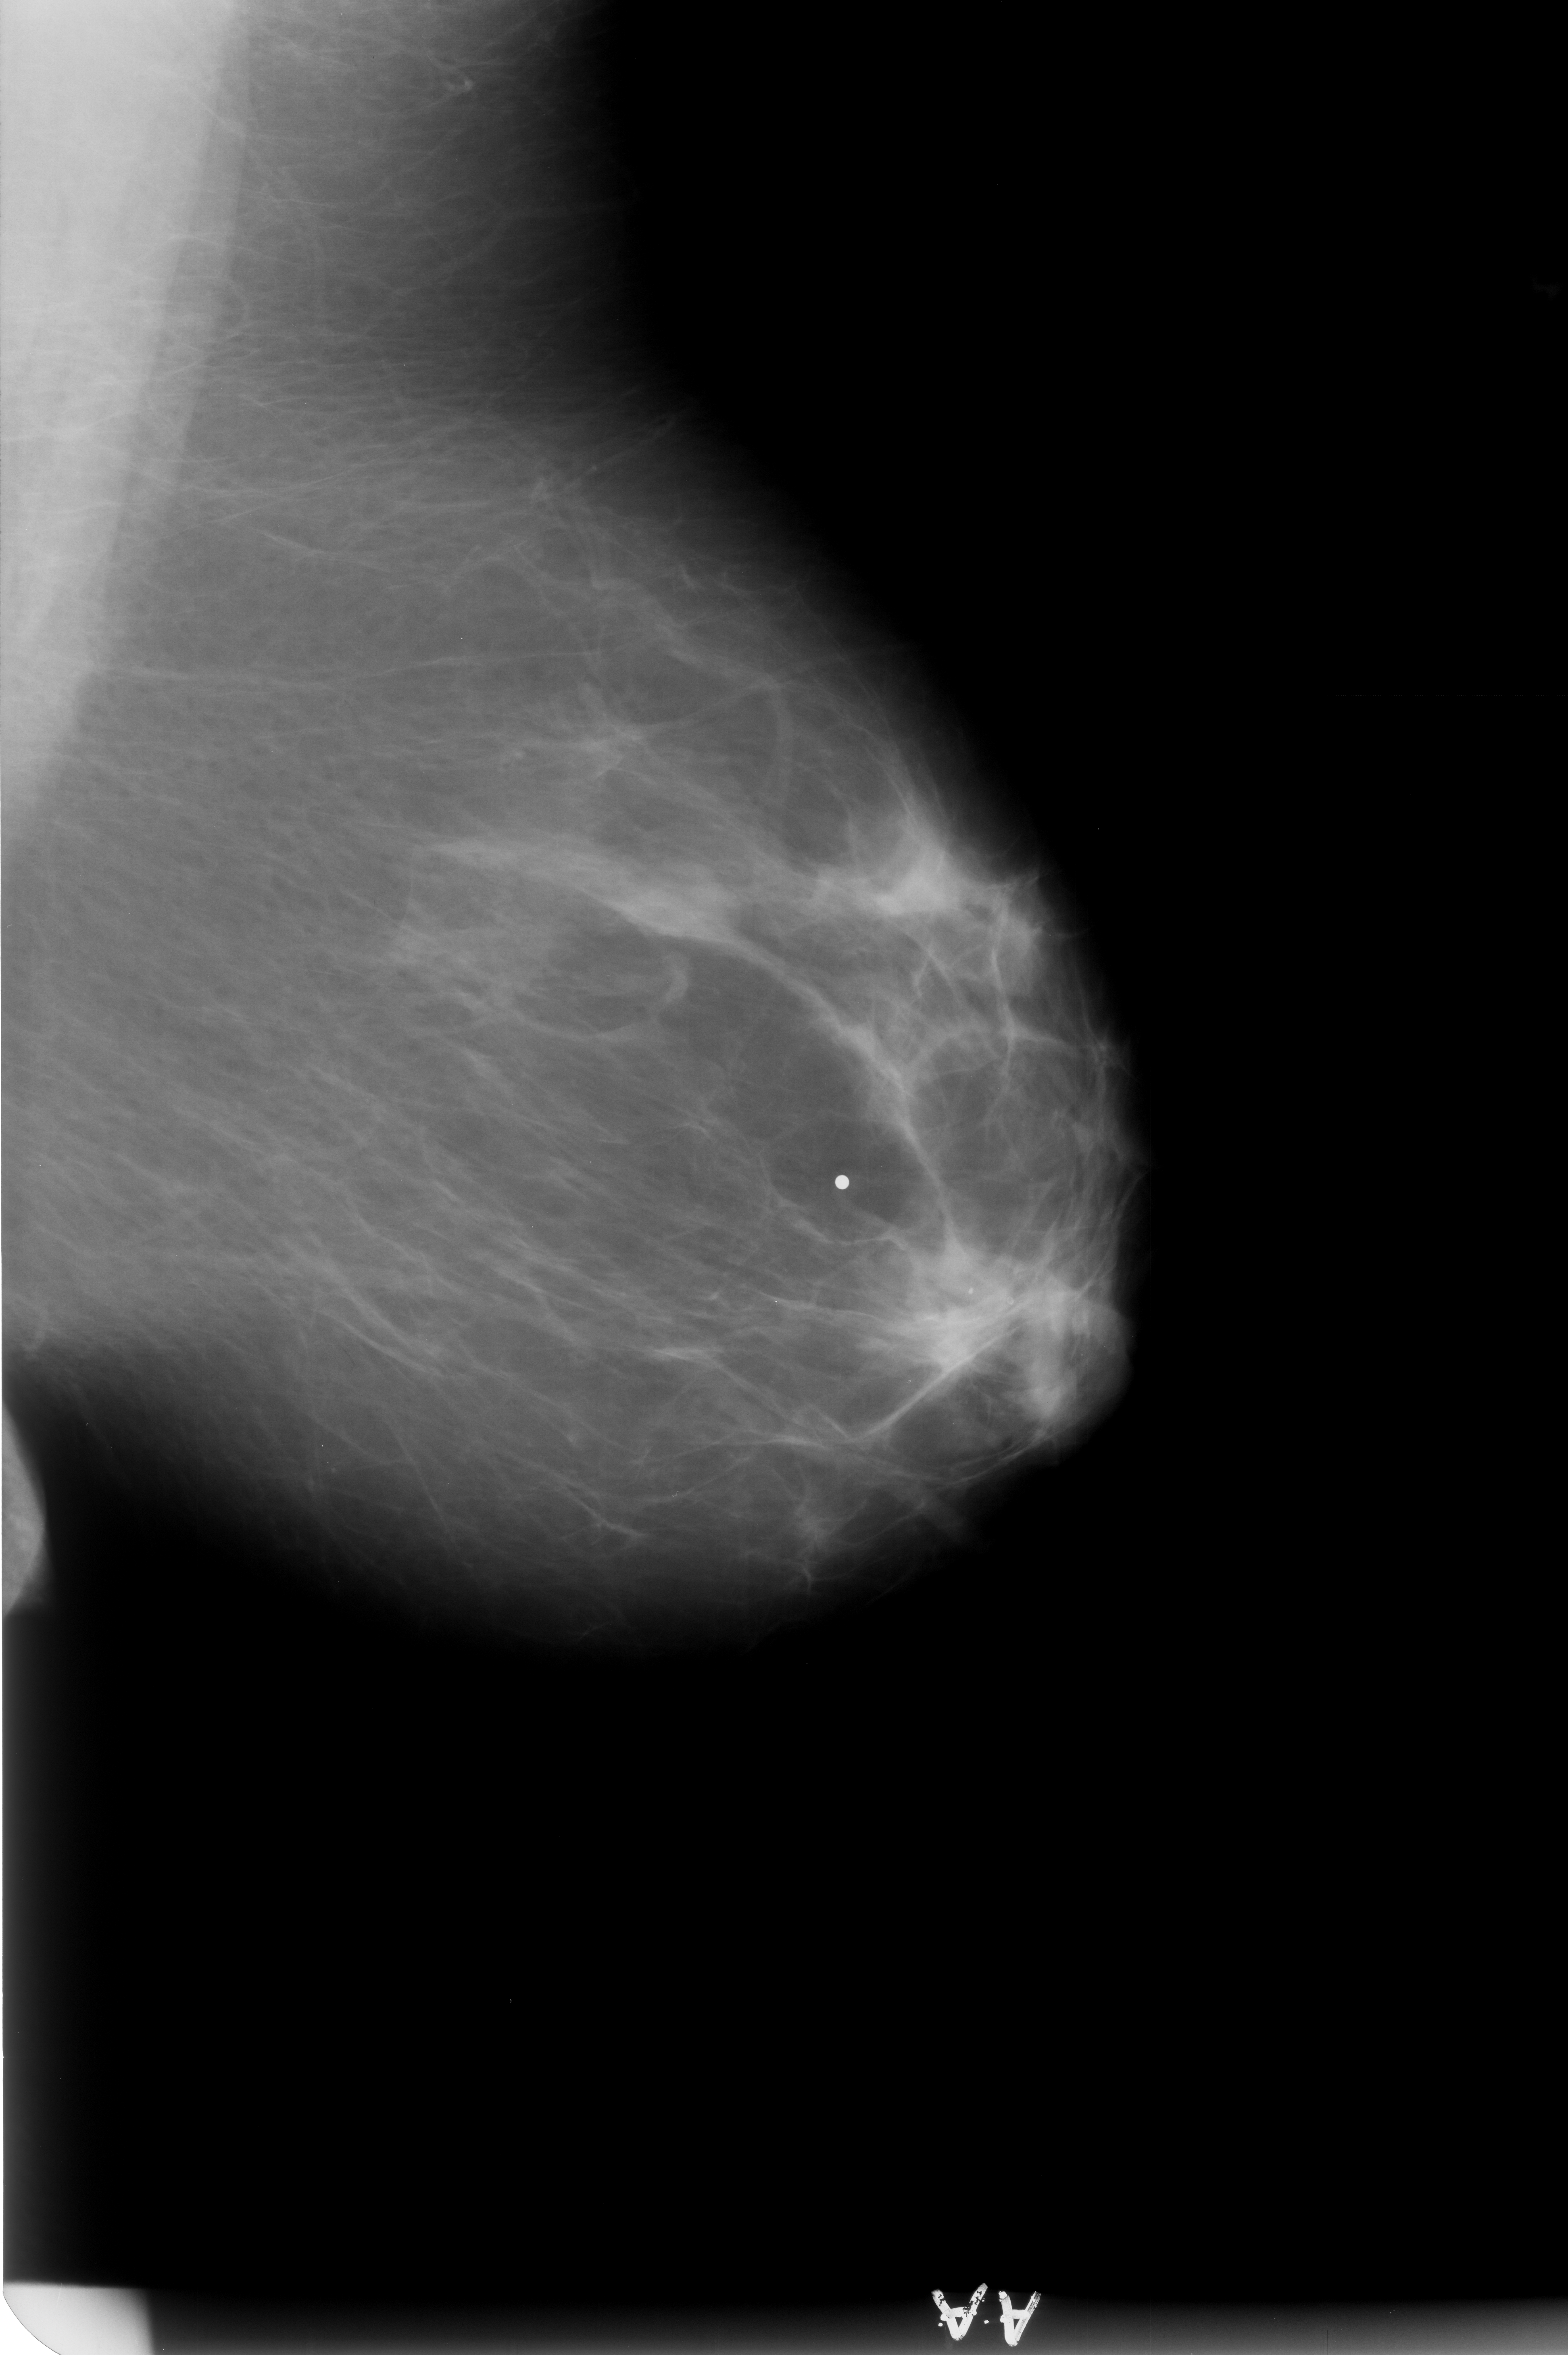
Scanned film-screen mammogram. Left breast. Mediolateral oblique (MLO) view. Breast composition: scattered fibroglandular densities (BI-RADS density category 2 of 4). 1568 × 2355 image matrix.
Expert-marked regions of interest on this image (one box per marked abnormality):
- Finding 1 of 2: calcifications, morphology lucent center / punctate; BI-RADS assessment category 2; benign; no additional work-up was recommended (outcome (as recorded, no biopsy): benign without callback): bounding box [x1, y1, x2, y2] px = [951, 1261, 988, 1314]
- Finding 2 of 2: calcifications, morphology lucent center / punctate; BI-RADS assessment category 2; benign; no additional work-up was recommended (outcome (as recorded, no biopsy): benign without callback): [984, 1271, 1024, 1307]